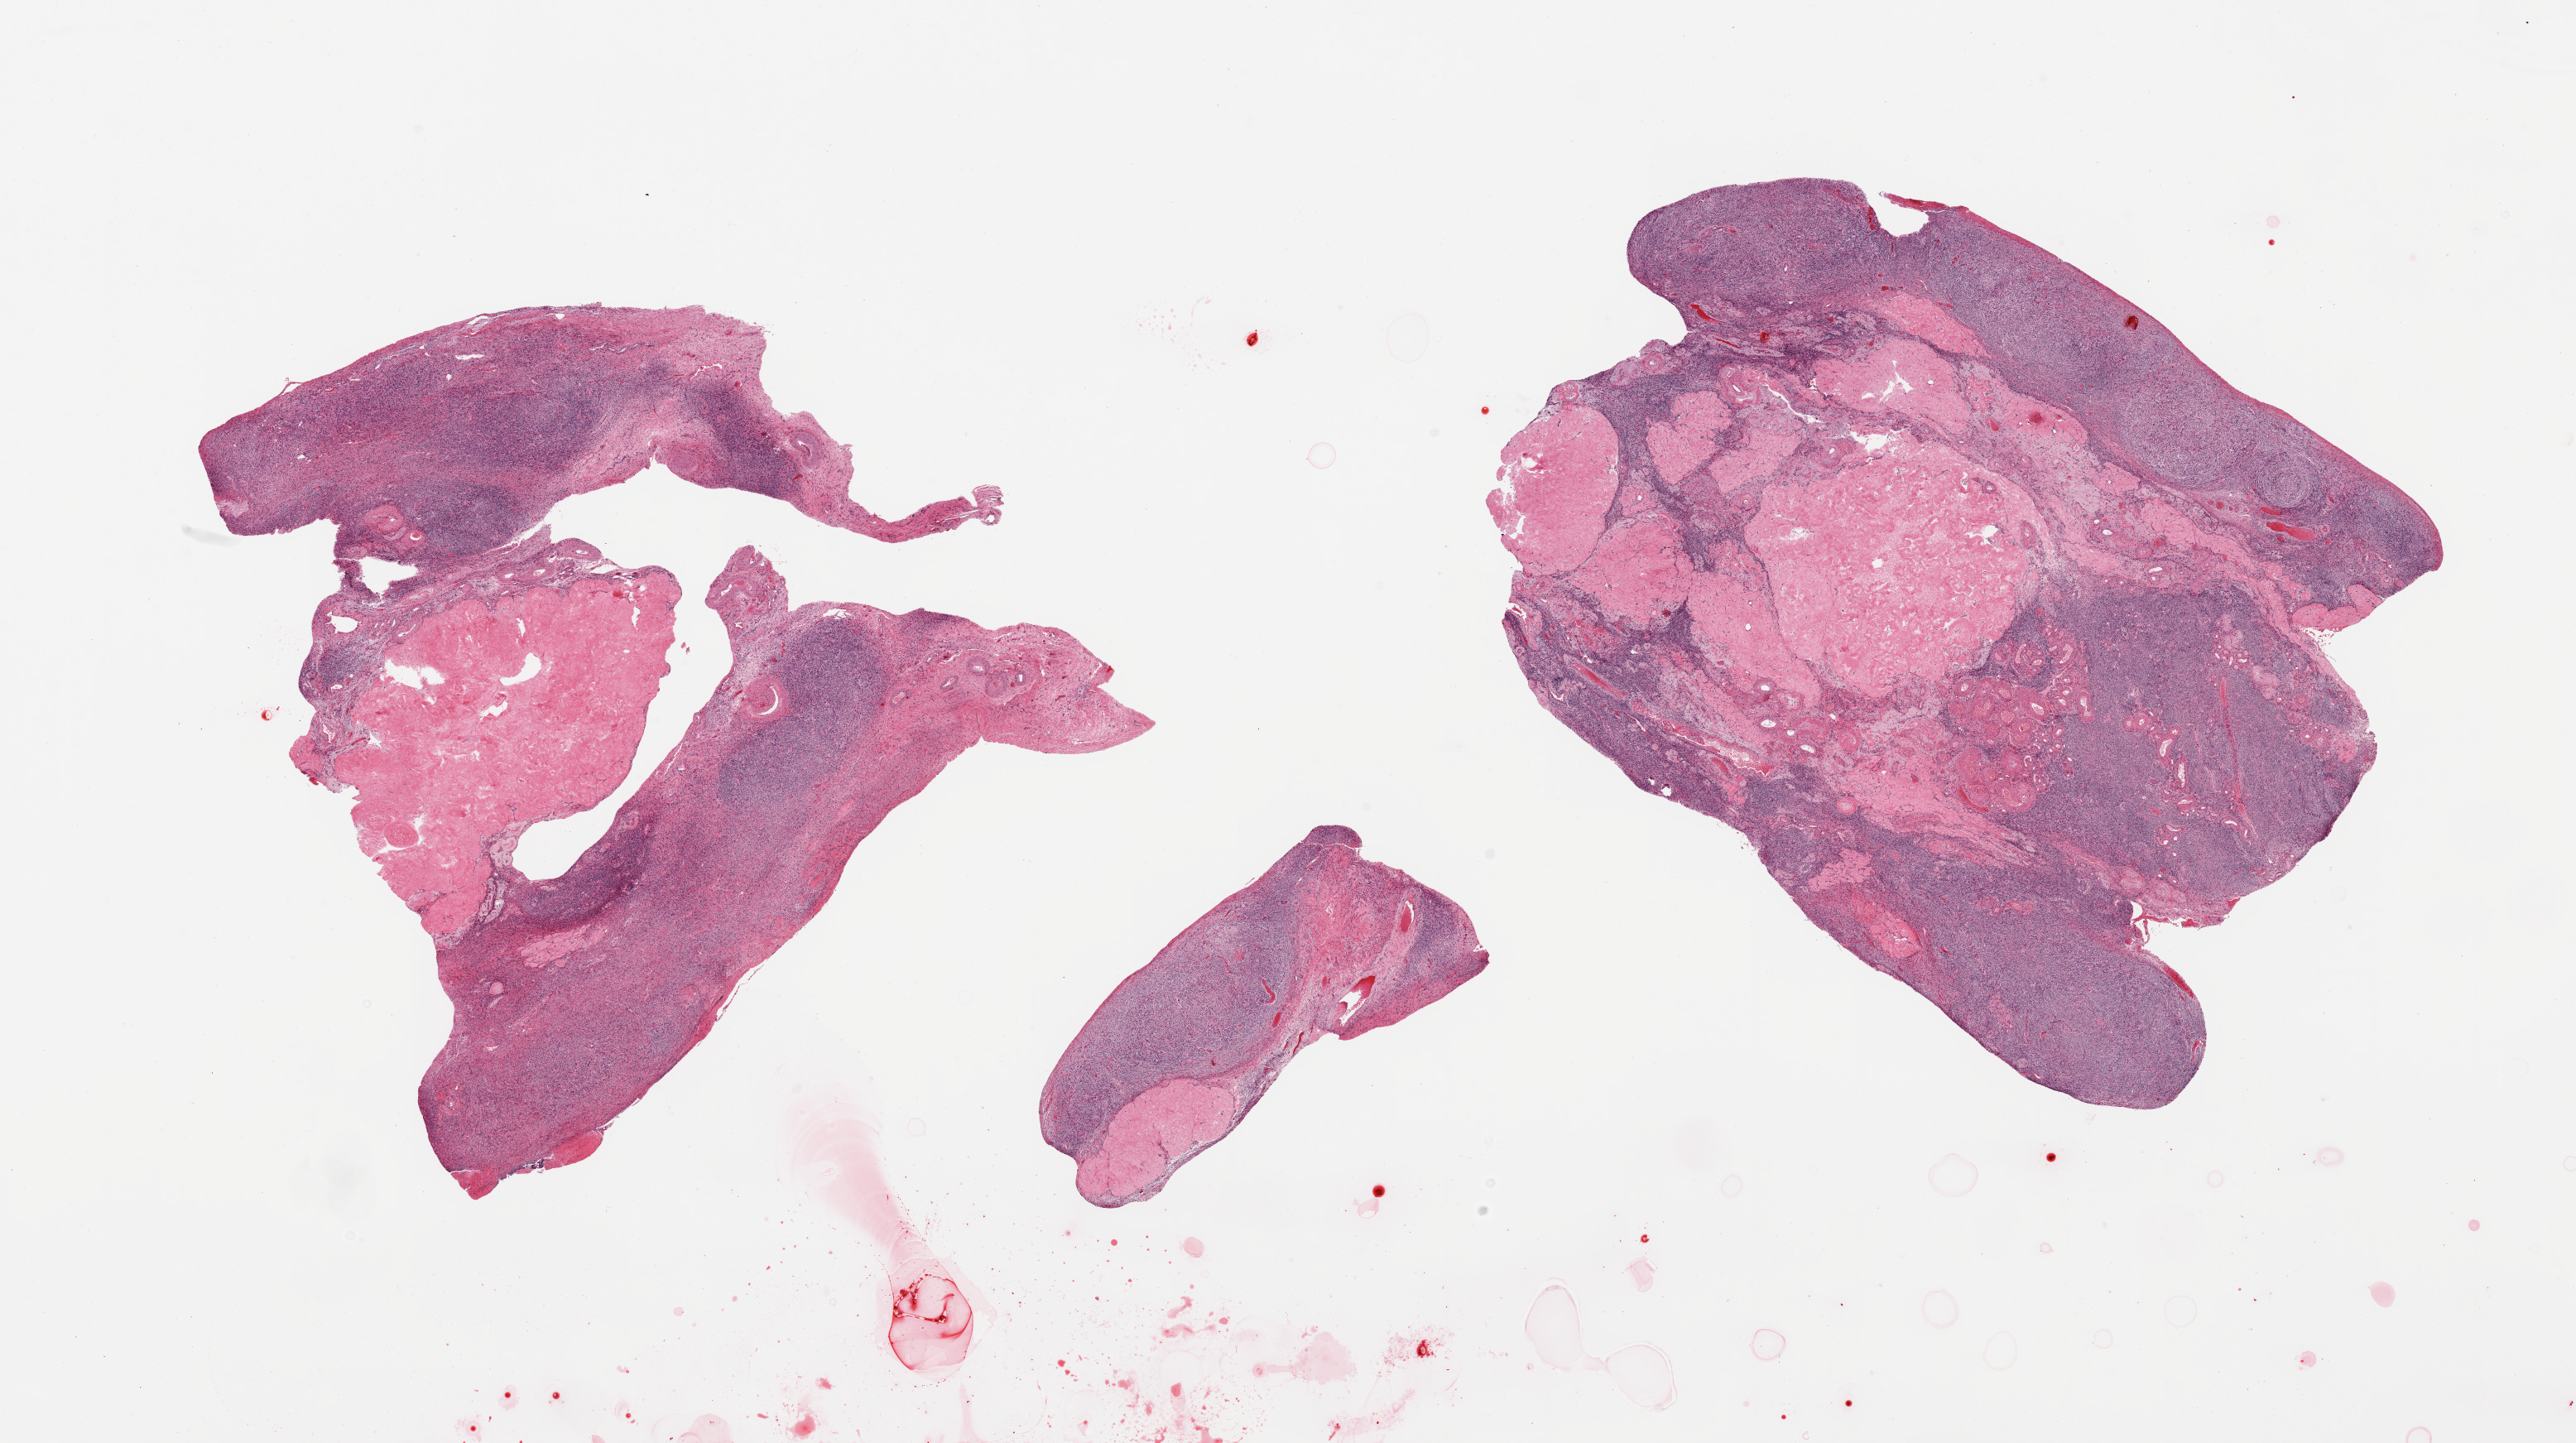
Digitized H&E-stained section, brightfield — a low-resolution overview of the entire scanned area, about 24.6 x 13.8 mm; PAXgene-fixed, paraffin-embedded tissue; target tissue: ovary; tissue donor sample. Female donor.
Reviewer comment on this tissue sample: 2 pieces, typical post menopausal atrophy, no abnormalities.